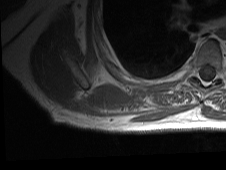
MRI of an extremity soft-tissue mass, one axial slice; slice 16 of 81 in the series (ordered by position); MR volume resampled by the dataset authors to the PET/CT grid (not the native acquisition matrix); 3.27 mm slice thickness; 226 × 170 image matrix. Male patient. From the clinical record (not read from this slice): histological type: pleiomorphic spindle cell undifferentiated; grade: high; site of the primary tumour: right parascapusular.
Outlined on this slice (expert contour drawn on MRI and transferred to this co-registered scan by the dataset authors):
- gross tumour volume including surrounding oedema: box from (x=121, y=97) to (x=191, y=121) px